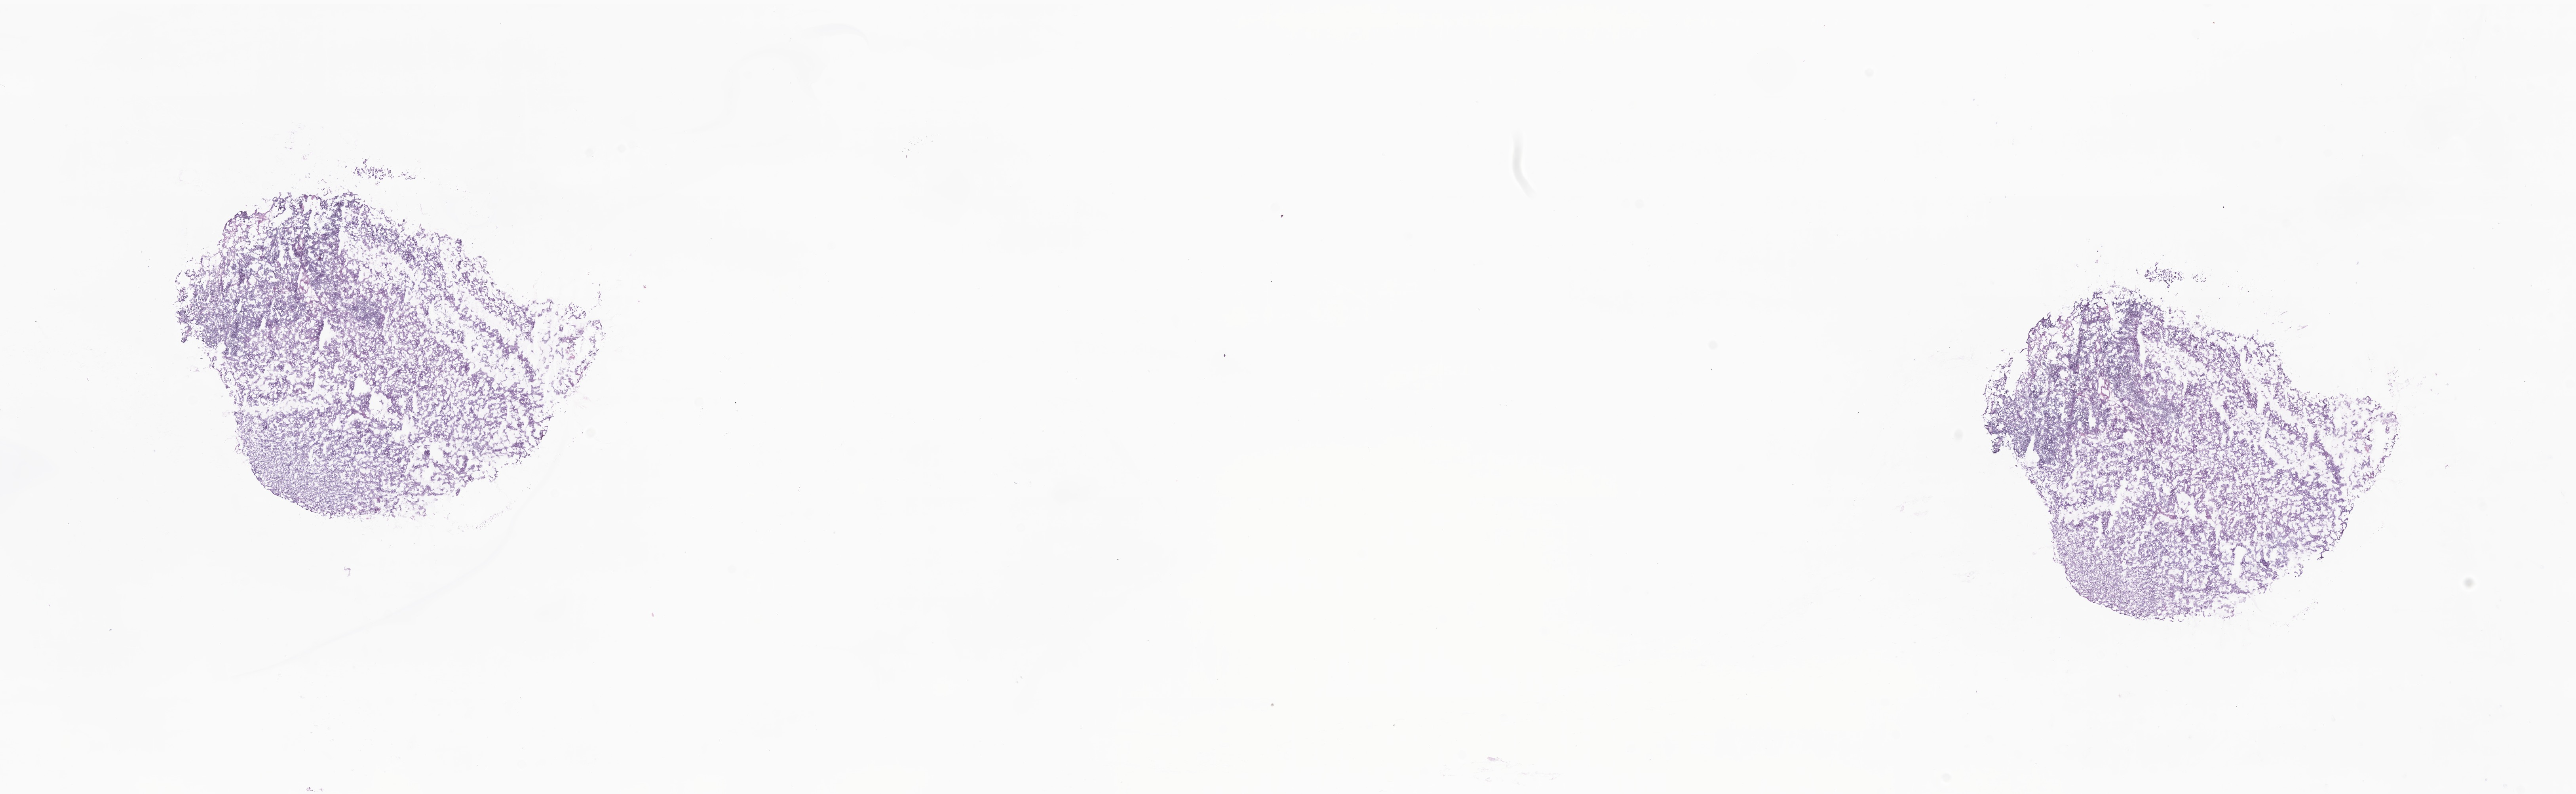
Digitized hematoxylin and eosin (H&E)-stained section — low-resolution overview of the scanned area, about 27.4 x 8.5 mm; frozen section; metastatic tumor tissue, resected from lymph nodes of inguinal region or leg. Patient: male, age at initial diagnosis 45 years. Pathologist review of this section (percent, as recorded): tumor cells 80%, tumor nuclei 80%, stromal cells 20%, necrosis 0%, normal cells 0%. Inflammatory infiltration, as recorded: lymphocyte infiltration 14%, monocyte infiltration 1%, neutrophil infiltration 1%.
Section: top of the tissue portion. Patient diagnosis (primary): Malignant melanoma, NOS.